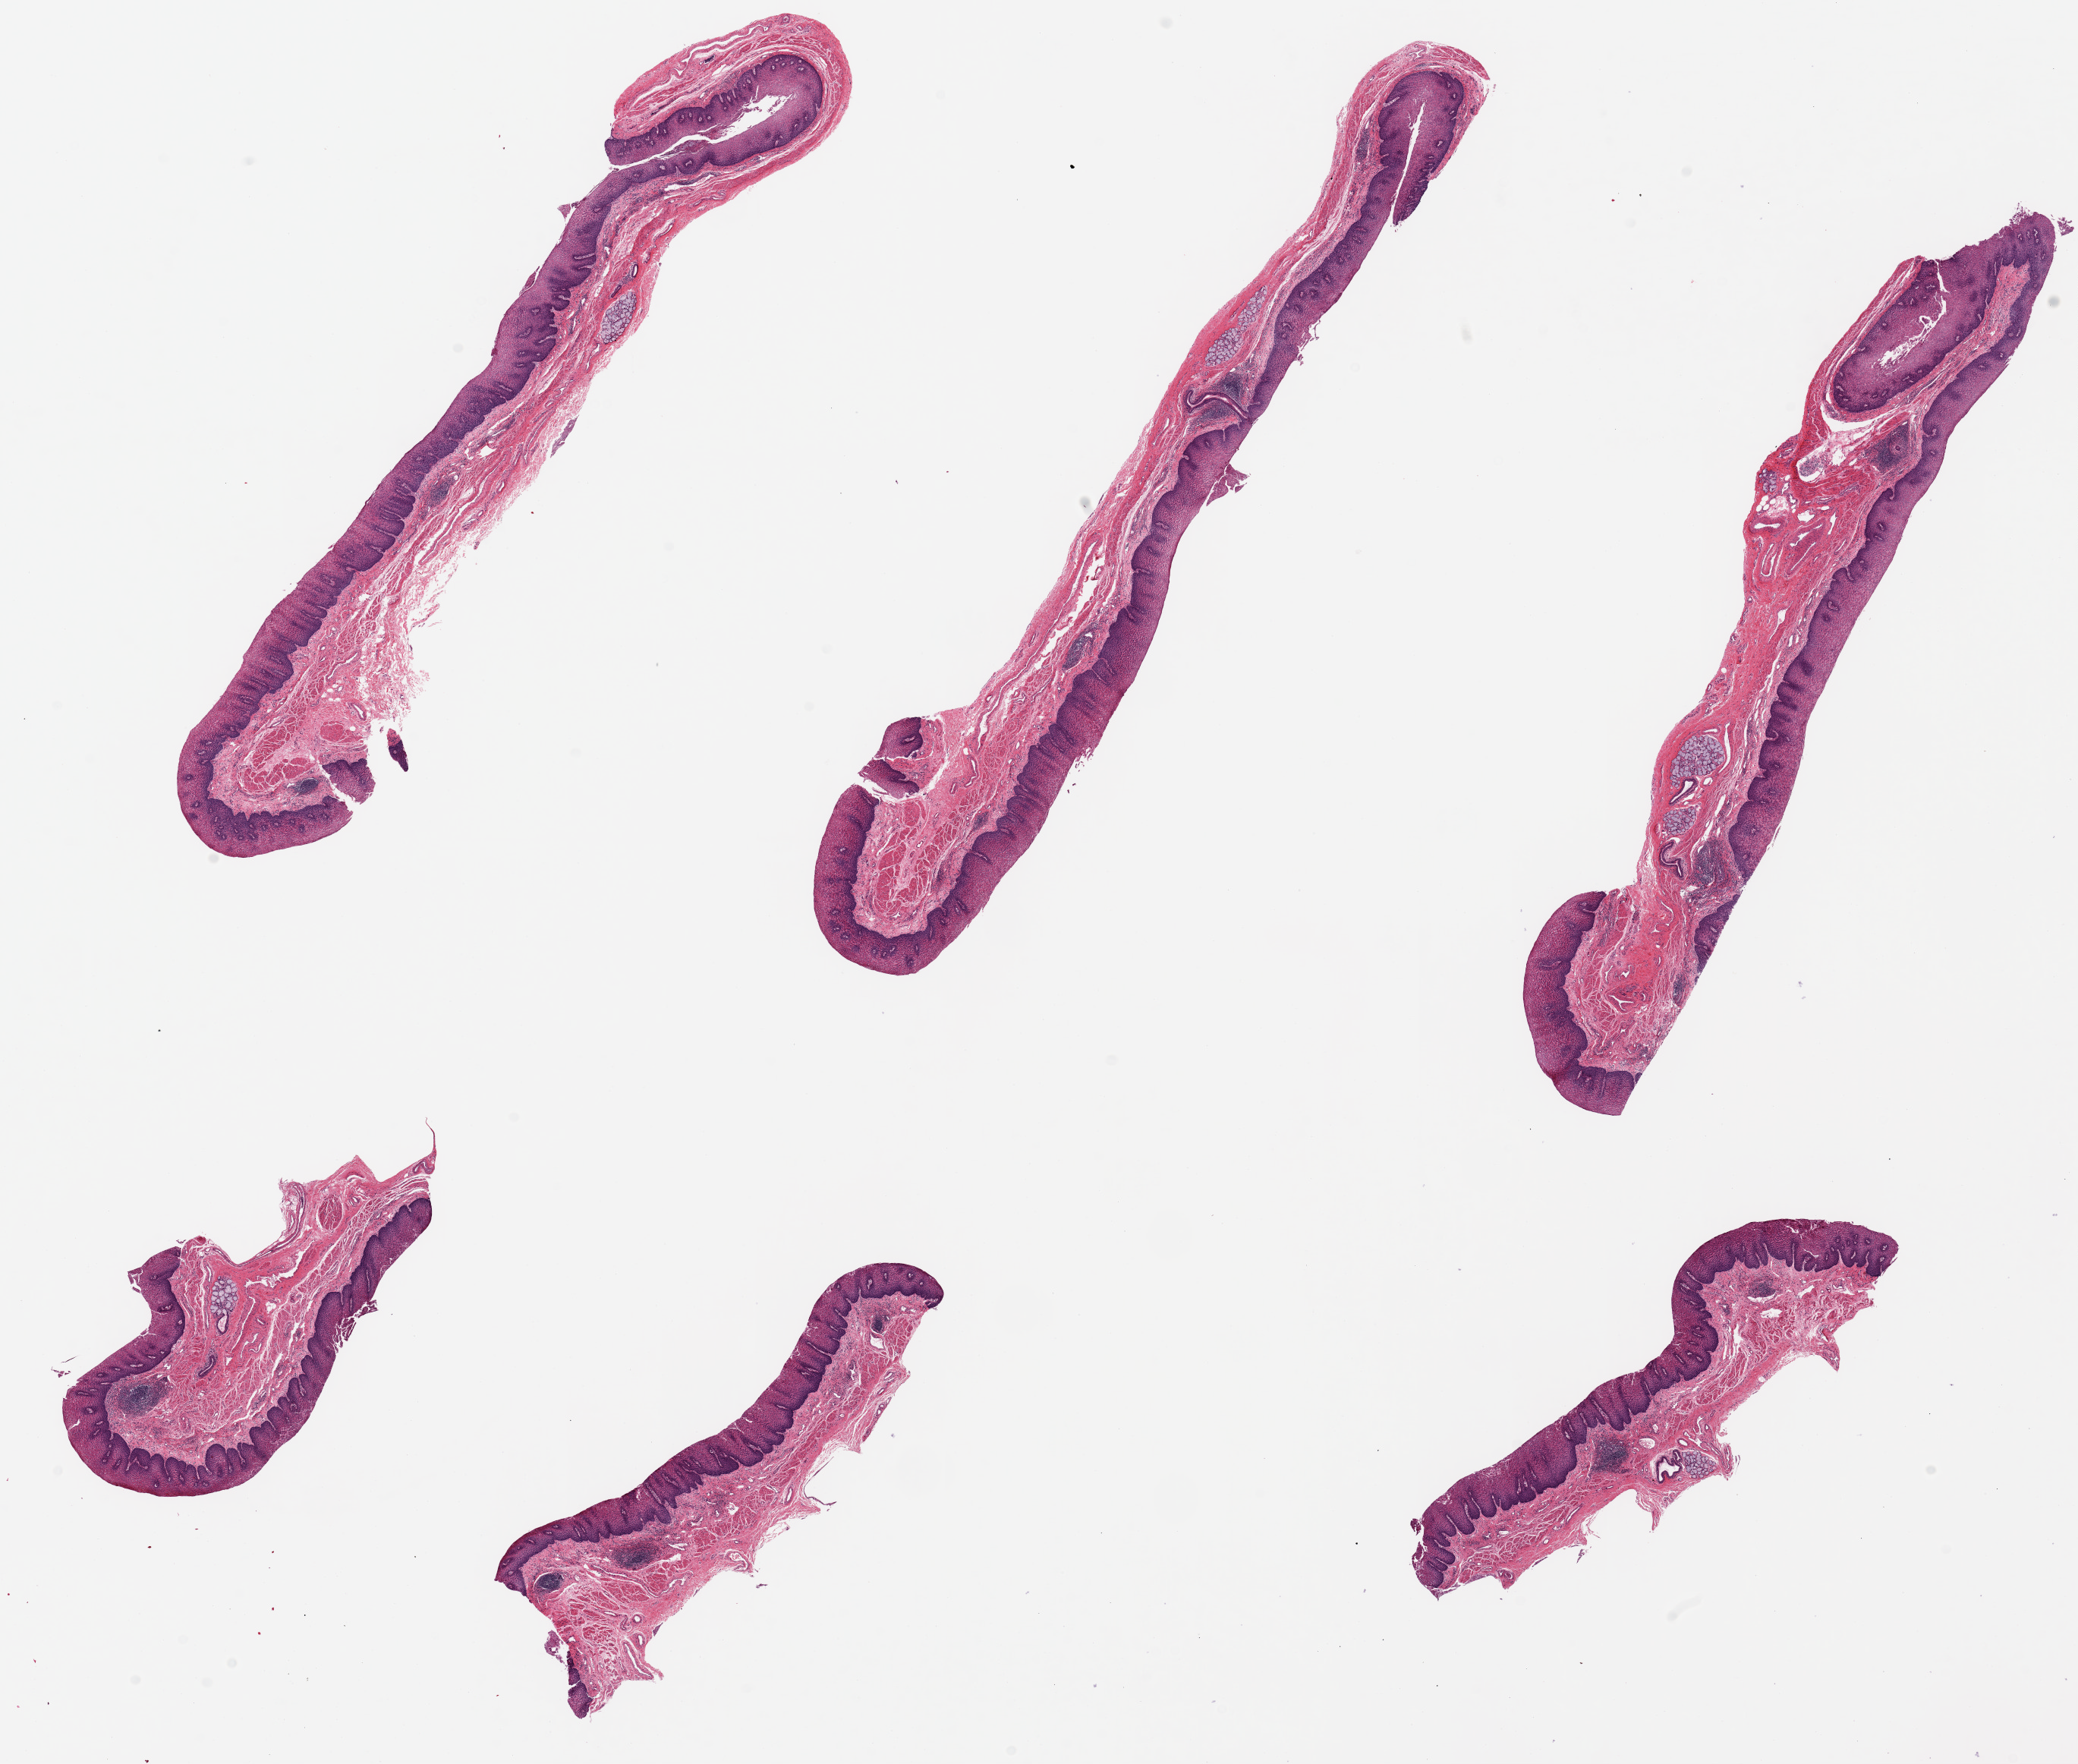
Whole-slide image, H&E stain, brightfield — shown as a low-resolution overview of the whole scanned area (about 21.7 x 18.4 mm, slide scanned at 20x); PAXgene-fixed paraffin-embedded (PFPE) section; target tissue: esophageal mucous membrane; donor tissue sample. Donor: male.
- pathologist's review note for this sample: 6 pieces ~10x1.5mm. Squamous mucosa, well preserved, ~30-40% of thickness